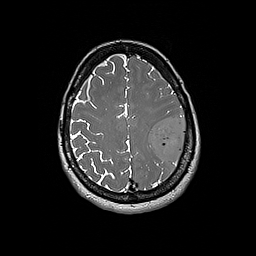
Brain MRI from a brain-tumour surgery series, one axial slice; slice 62 of 192 in the series (ordered by position); 1 mm slice thickness; 256 × 256 image matrix. Case-level facts recorded for this patient, not image findings: histopathology: Glioblastoma; WHO grade: 4; IDH mutation: no.
Structures marked on this image (outlined manually by an expert reader):
- tumour: box from (x=150, y=114) to (x=186, y=164) px